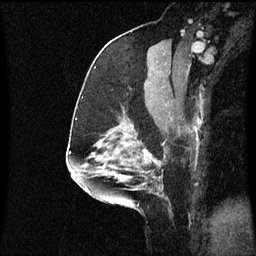
Breast MRI (dynamic contrast-enhanced), one sagittal slice; position 35 of 60 along the scan axis; dynamic contrast-enhanced series, image 2 of 3 at this slice position (ordered by acquisition); 1.5 T; TE 4.2 ms, TR 8.9 ms; 256 × 256 image matrix, field of view 200 × 200 mm. Female patient, age 58 years. From the clinical record (not read from this slice): setting: breast cancer imaged before/during neoadjuvant chemotherapy; receptor status: triple-negative.
Outlined on this slice (semi-automatically segmented with operator editing):
- analysis volume of interest (the breast-tissue region the enhancement analysis was run in; not a lesion): box from (x=104, y=118) to (x=171, y=179) px
- tumour enhancement mask (voxels above the 70 % enhancement threshold inside the analysis volume of interest): (x=116, y=150)–(x=155, y=179)